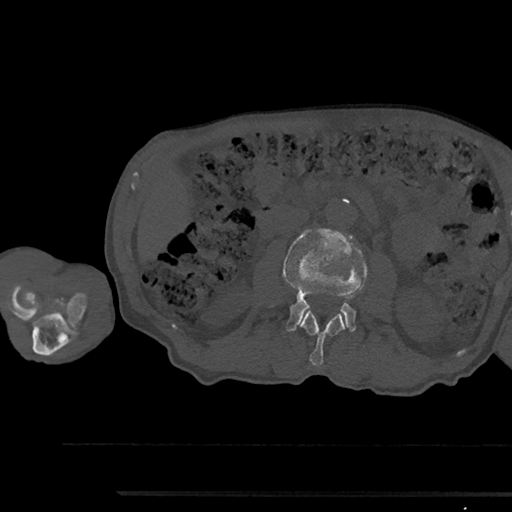
CT including the spine, one axial slice; position 524 of 797 along the scan axis; reconstruction kernel Br40s/3; bone window (W 1800 / L 400 HU); 0.5 mm slice thickness; 512 × 512 image matrix, field of view 367 × 367 mm. Patient: male, 79 years. Case-level facts recorded for this patient, not image findings: primary cancer: prostate.
Outlined on this slice (semi-automatically segmented with operator editing):
- L2 vertebra: bounding box <300,310,345,366> (left, top, right, bottom; pixels)
- L3 vertebra: <284,229,368,332>